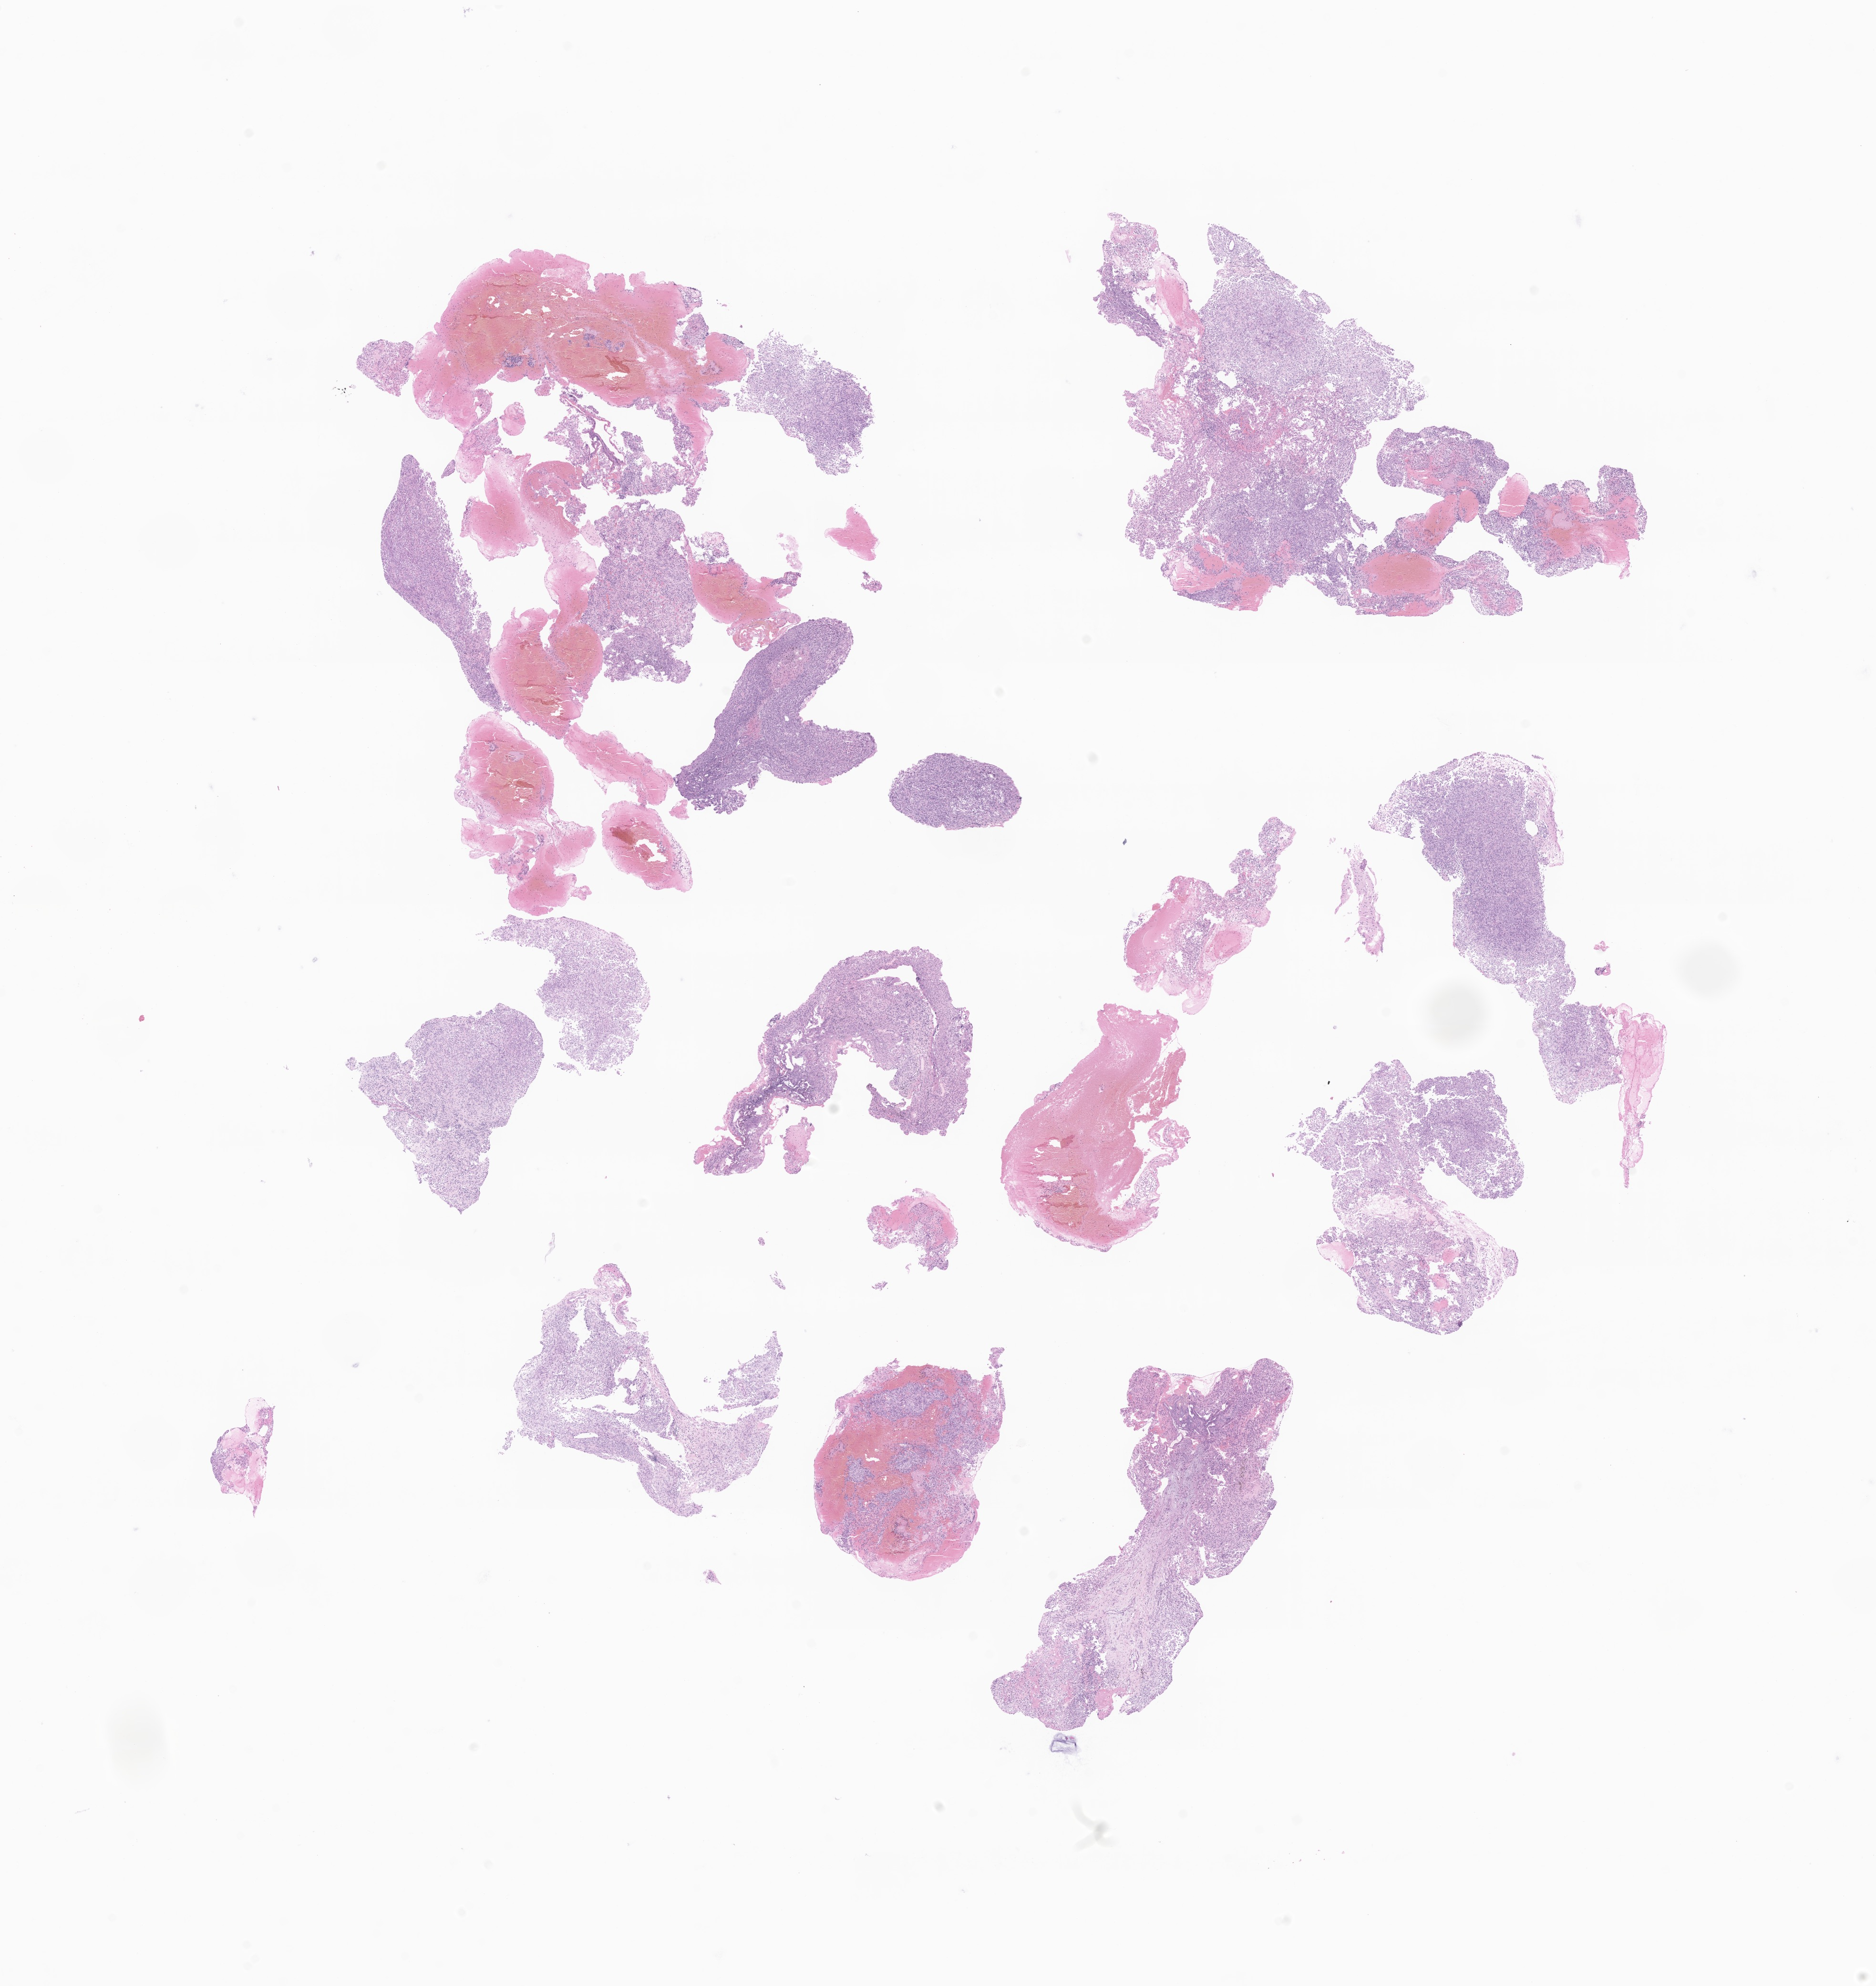
Whole-slide image, haematoxylin and eosin stain of tumor tissue from the brain, low-resolution overview of the scanned area, about 16.6 x 17.6 mm; FFPE section. Female patient, age 53 months (4 years 5 months).
Diagnosis: Atypical teratoid/rhabdoid tumor.